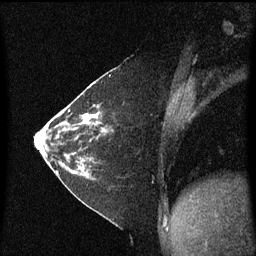
Breast MRI (dynamic contrast-enhanced), one sagittal slice. Position 26 of 60 along the scan axis. Dynamic contrast-enhanced series, image 2 of 3 at this slice position (ordered by acquisition). 1.5 T. TE 4.2 ms, TR 8.4 ms. 2 mm slice thickness. 256 × 256 image matrix, field of view 200 × 200 mm. Patient: female, 36 years. Case-level facts recorded for this patient, not image findings: setting: breast cancer imaged before/during neoadjuvant chemotherapy; receptor status: HR-positive, HER2-negative.
Annotated regions visible in this slice (semi-automatically segmented with operator editing):
- analysis volume of interest (the breast-tissue region the enhancement analysis was run in; not a lesion): bounding box (x1, y1, x2, y2) in pixels: (66, 102, 108, 179)
- tumour enhancement mask (voxels above the 70 % enhancement threshold inside the analysis volume of interest): (83, 112, 108, 133)